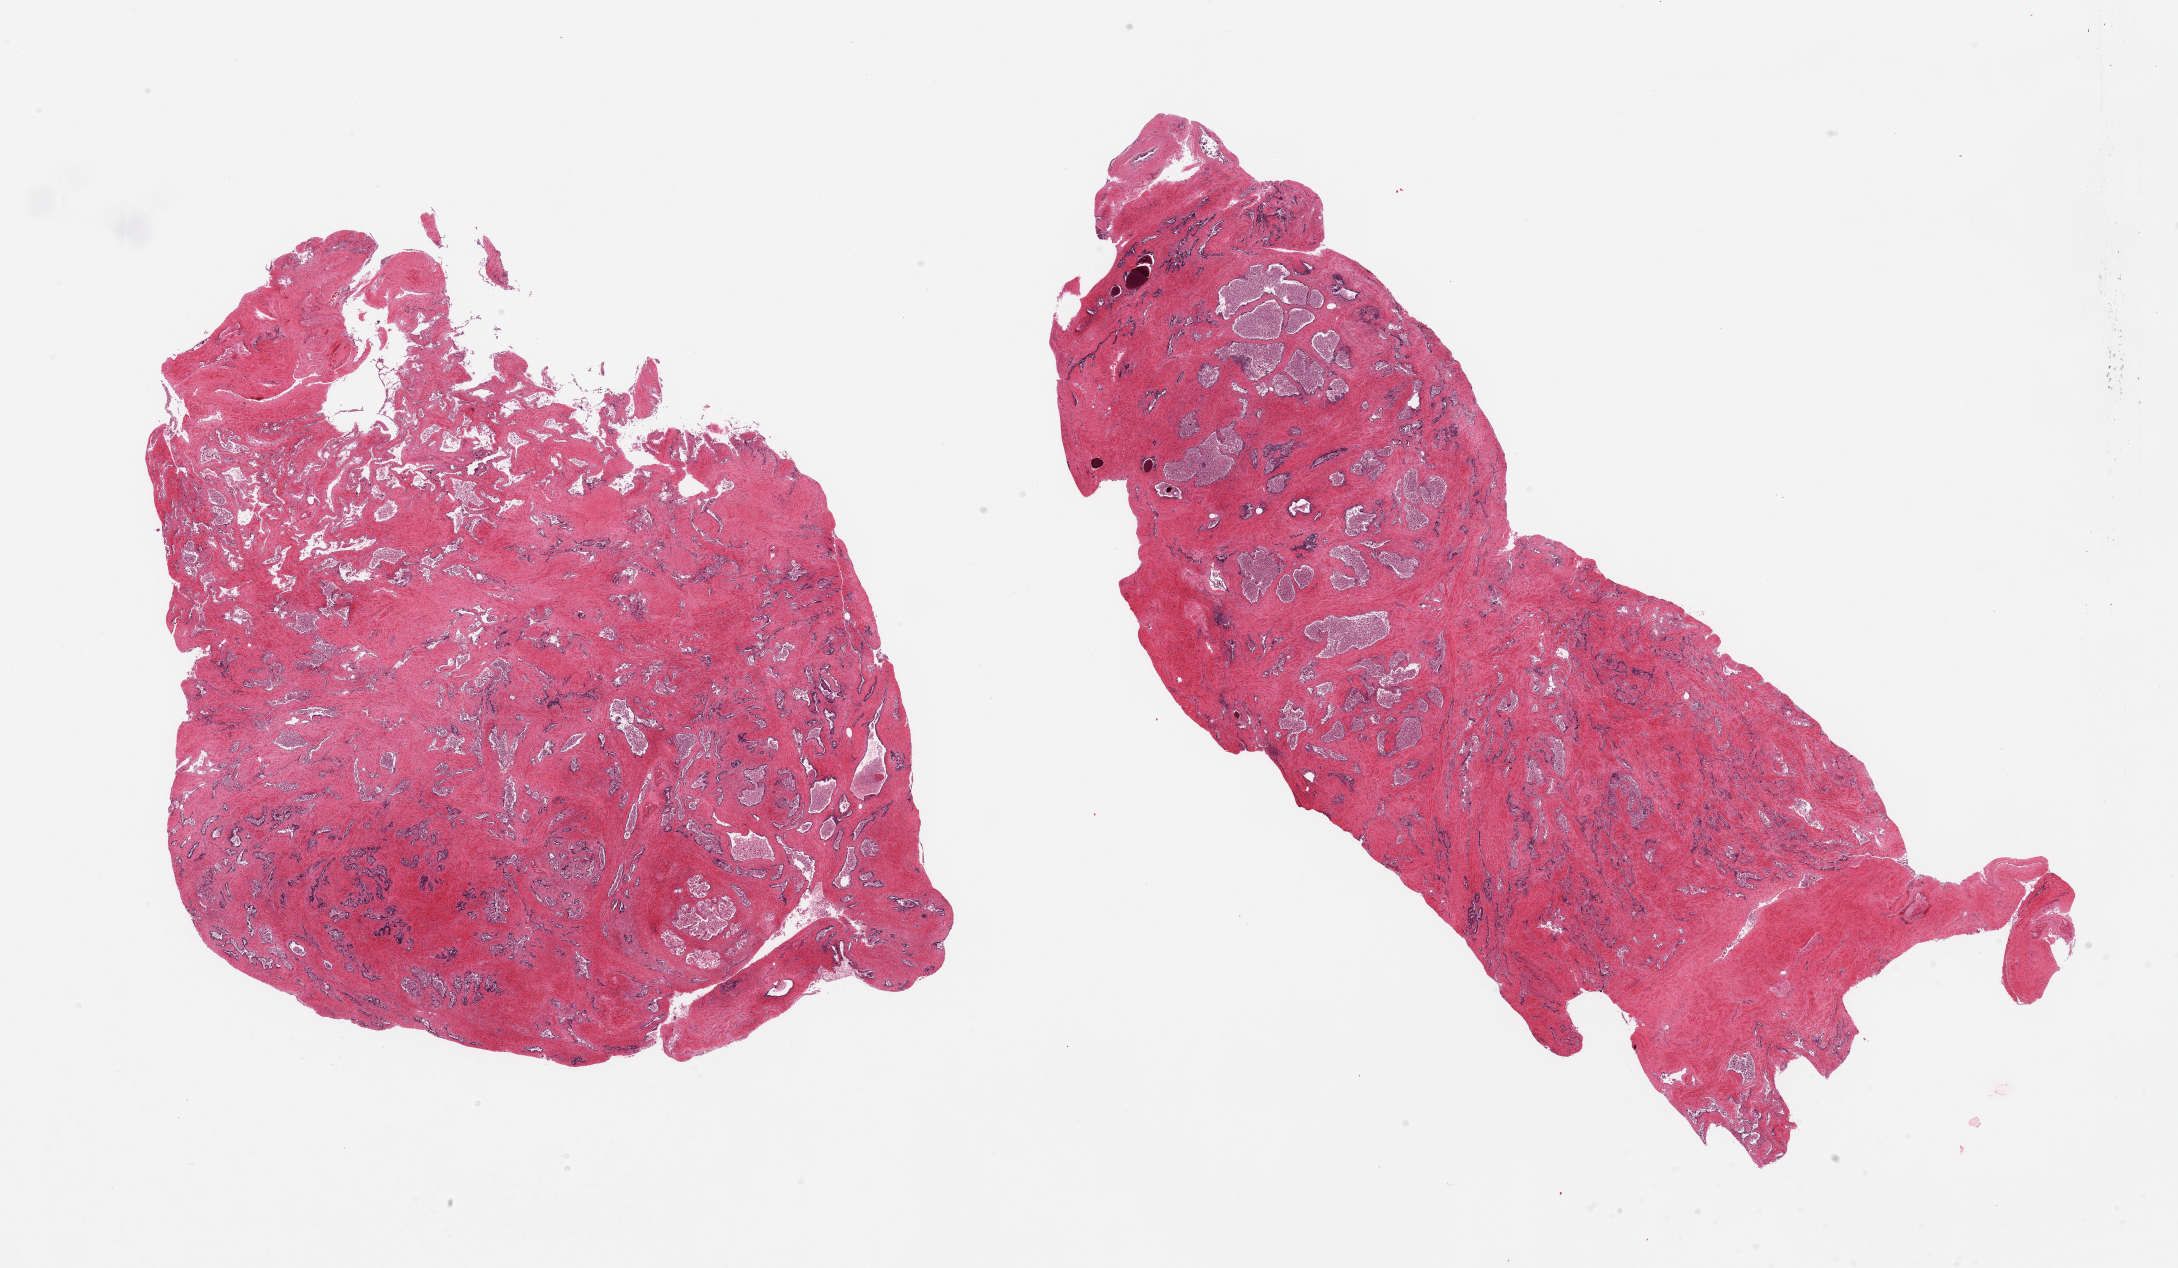
Haematoxylin and eosin whole-slide image, shown as a low-resolution overview of the whole scanned area (about 34.5 x 20.1 mm). PAXgene-fixed, paraffin-embedded tissue. Sampled site (target tissue): prostate. Tissue donor sample. Donor: male.
Reviewer comment on this tissue sample: 2 pieces, glandular component markedly autolyzed, has glandular hyperplastic pattern.